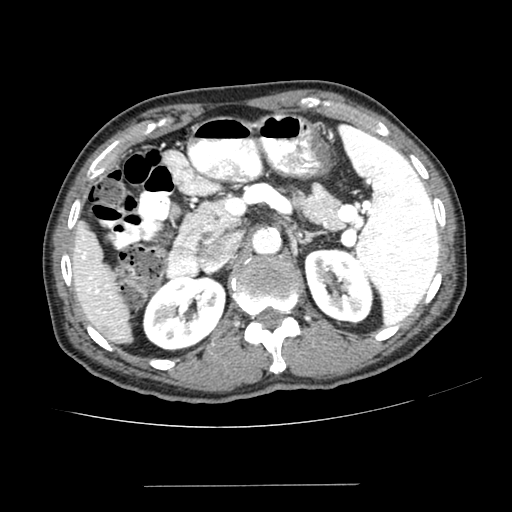
Contrast-enhanced abdominal CT (liver protocol), one axial slice; slice 141 of 187 in the series (ordered by position); 100 kVp; one of 2 acquisitions stored at this slice position; soft-tissue window (W 400 / L 40 HU); 2.5 mm slice thickness; 512 × 512 image matrix, field of view 360 × 360 mm. From the clinical record (not read from this slice): diagnosis: hepatocellular carcinoma (patient treated with transarterial chemoembolisation; whether this scan precedes or follows treatment is not stated here); TNM stage (as recorded): Stage-I; Child-Pugh class: A; tumour nodularity: uninodular; tumour size: 1.6 cm.
Structures marked on this image (semi-automatically segmented with operator editing):
- liver parenchyma outside the tumour (the mass and vessels are separate outlines, so this box may not span the whole liver): box from (x=70, y=220) to (x=132, y=342) px
- liver vessels: (x=77, y=237)–(x=111, y=314)